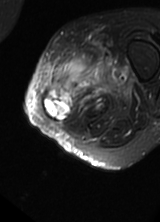
MRI of an extremity soft-tissue mass, one axial slice; position 15 of 69 along the scan axis; T2-weighted fat-saturated; MR volume resampled by the dataset authors to the PET/CT grid (not the native acquisition matrix); 3.27 mm slice thickness; 160 × 222 image matrix, field of view 156 × 217 mm. Female patient. From the clinical record (not read from this slice): histological type: pleomorphic leiomyosarcoma; grade: high; site of the primary tumour: left thigh.
Outlined on this slice (expert contour drawn on MRI and transferred to this co-registered scan by the dataset authors):
- gross tumour volume including surrounding oedema: bounding box (x1, y1, x2, y2) in pixels: (41, 52, 129, 121)
- gross tumour volume (mass): (43, 89, 72, 121)